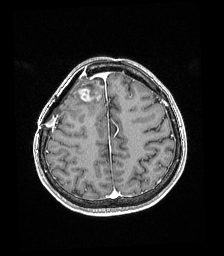
Brain MRI from a brain-tumour surgery series, one axial slice. T1-weighted post-contrast. 224 × 256 image matrix. Case-level facts recorded for this patient, not image findings: histopathology: Astrocytoma; WHO grade: 4; IDH mutation: yes; tumour location: Right superficial frontal.
Outlined on this slice (manually delineated by an expert):
- tumour: box from (x=76, y=82) to (x=102, y=102) px